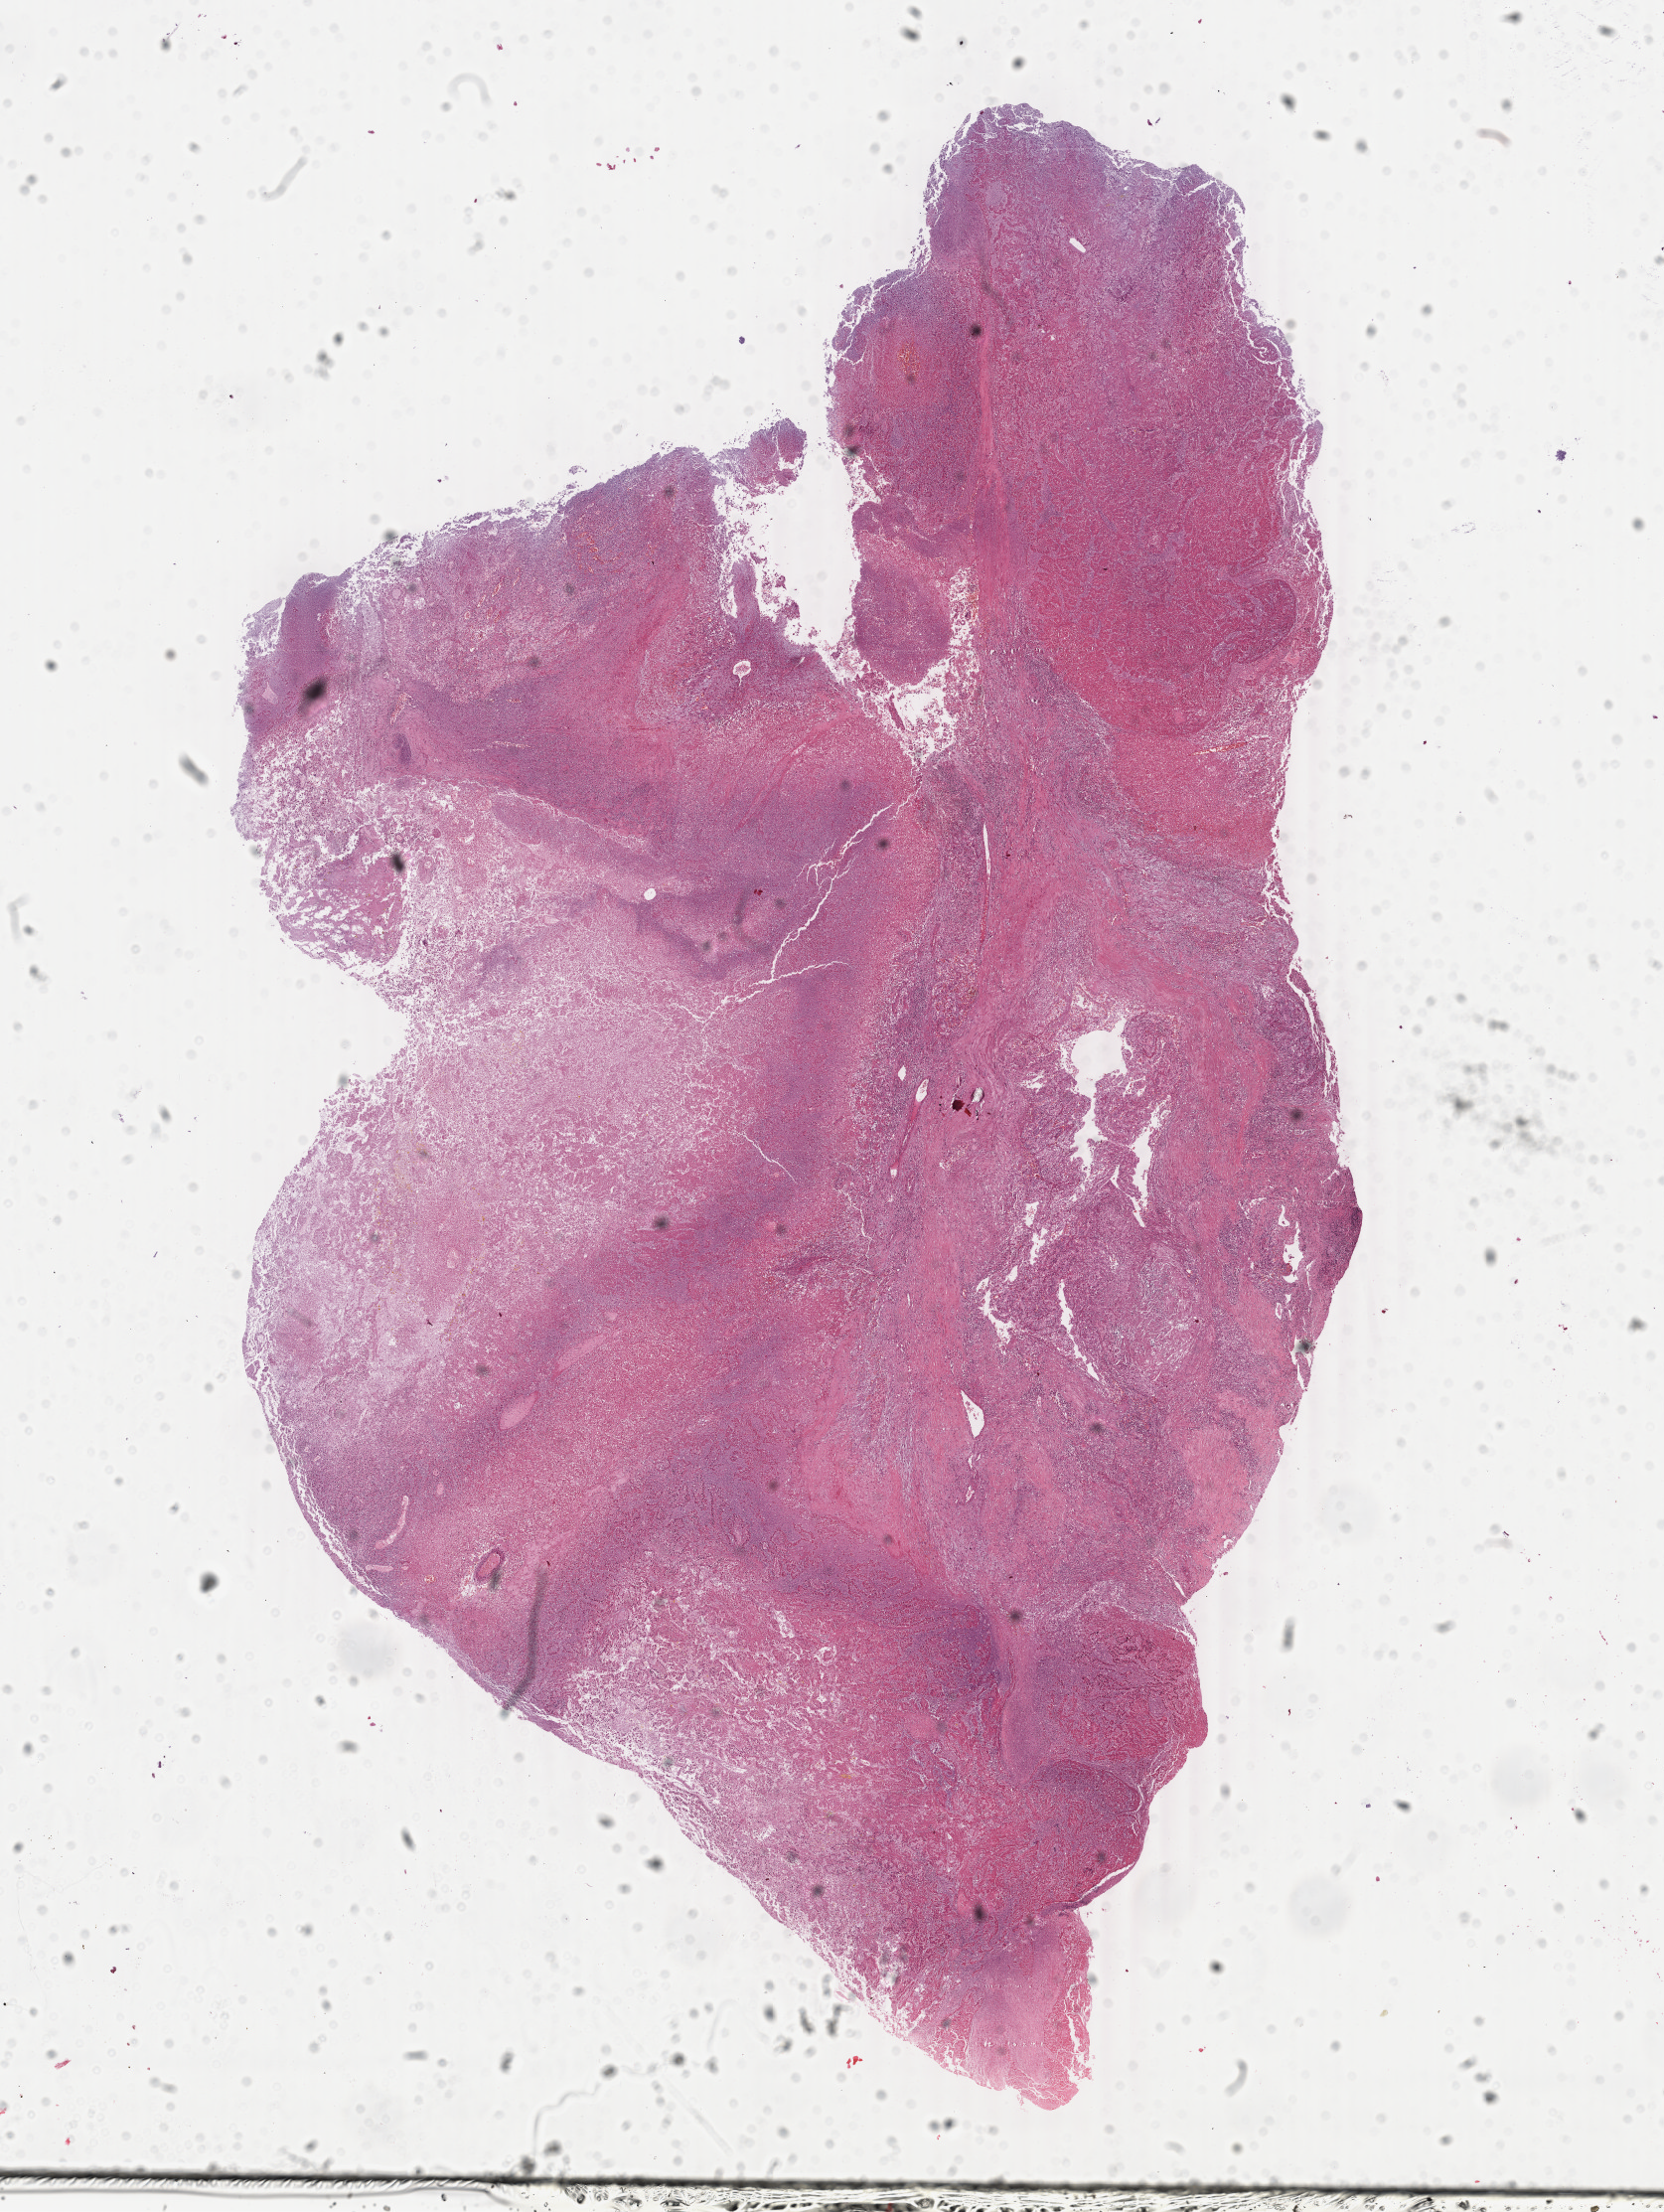
Digitized Hematoxylin and eosin (H&E) stained tissue section (whole slide), shown as a low-resolution overview of the whole scanned area (about 13.3 x 17.7 mm, acquisition: 40x scan); formalin-fixed paraffin-embedded (FFPE) diagnostic section; primary tumour sample from the kidney. Female patient; age at initial diagnosis 37 years.
AJCC pathologic stage: III (7th edition). Diagnosis: Papillary adenocarcinoma, NOS. Lymph nodes positive (case pathology): 2 of 2 examined.